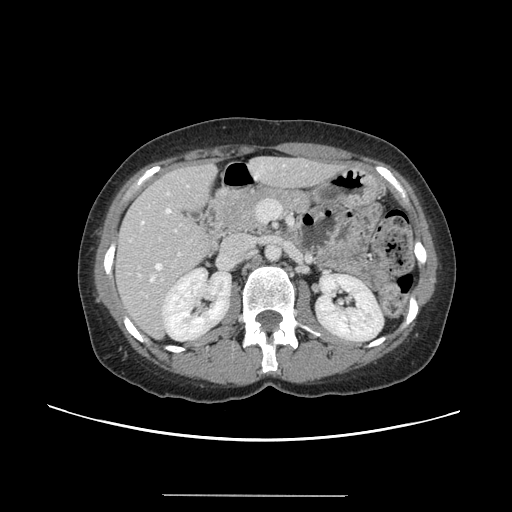
Contrast-enhanced abdominal CT, one axial slice. Position 67 of 144 along the scan axis. 120 kVp. Intravenous contrast given. Soft-tissue window (W 400 / L 40 HU). 2.5 mm slice thickness. 512 × 512 image matrix, field of view 380 × 380 mm. Female patient, age 53 years. From the clinical record (not read from this slice): diagnosis: colorectal cancer liver metastases, imaged before liver resection; multiple liver metastases: yes; largest metastasis: 1.1 cm; disease in both lobes: no.
Annotated regions visible in this slice (expert manual segmentation):
- hepatic veins: bounding box (x1, y1, x2, y2) in pixels: (139, 193, 170, 281)
- liver: (118, 159, 336, 336)
- planned liver remnant (the part of the liver to remain after resection): (118, 159, 325, 305)
- portal vein (with intrahepatic branches): (146, 199, 282, 297)